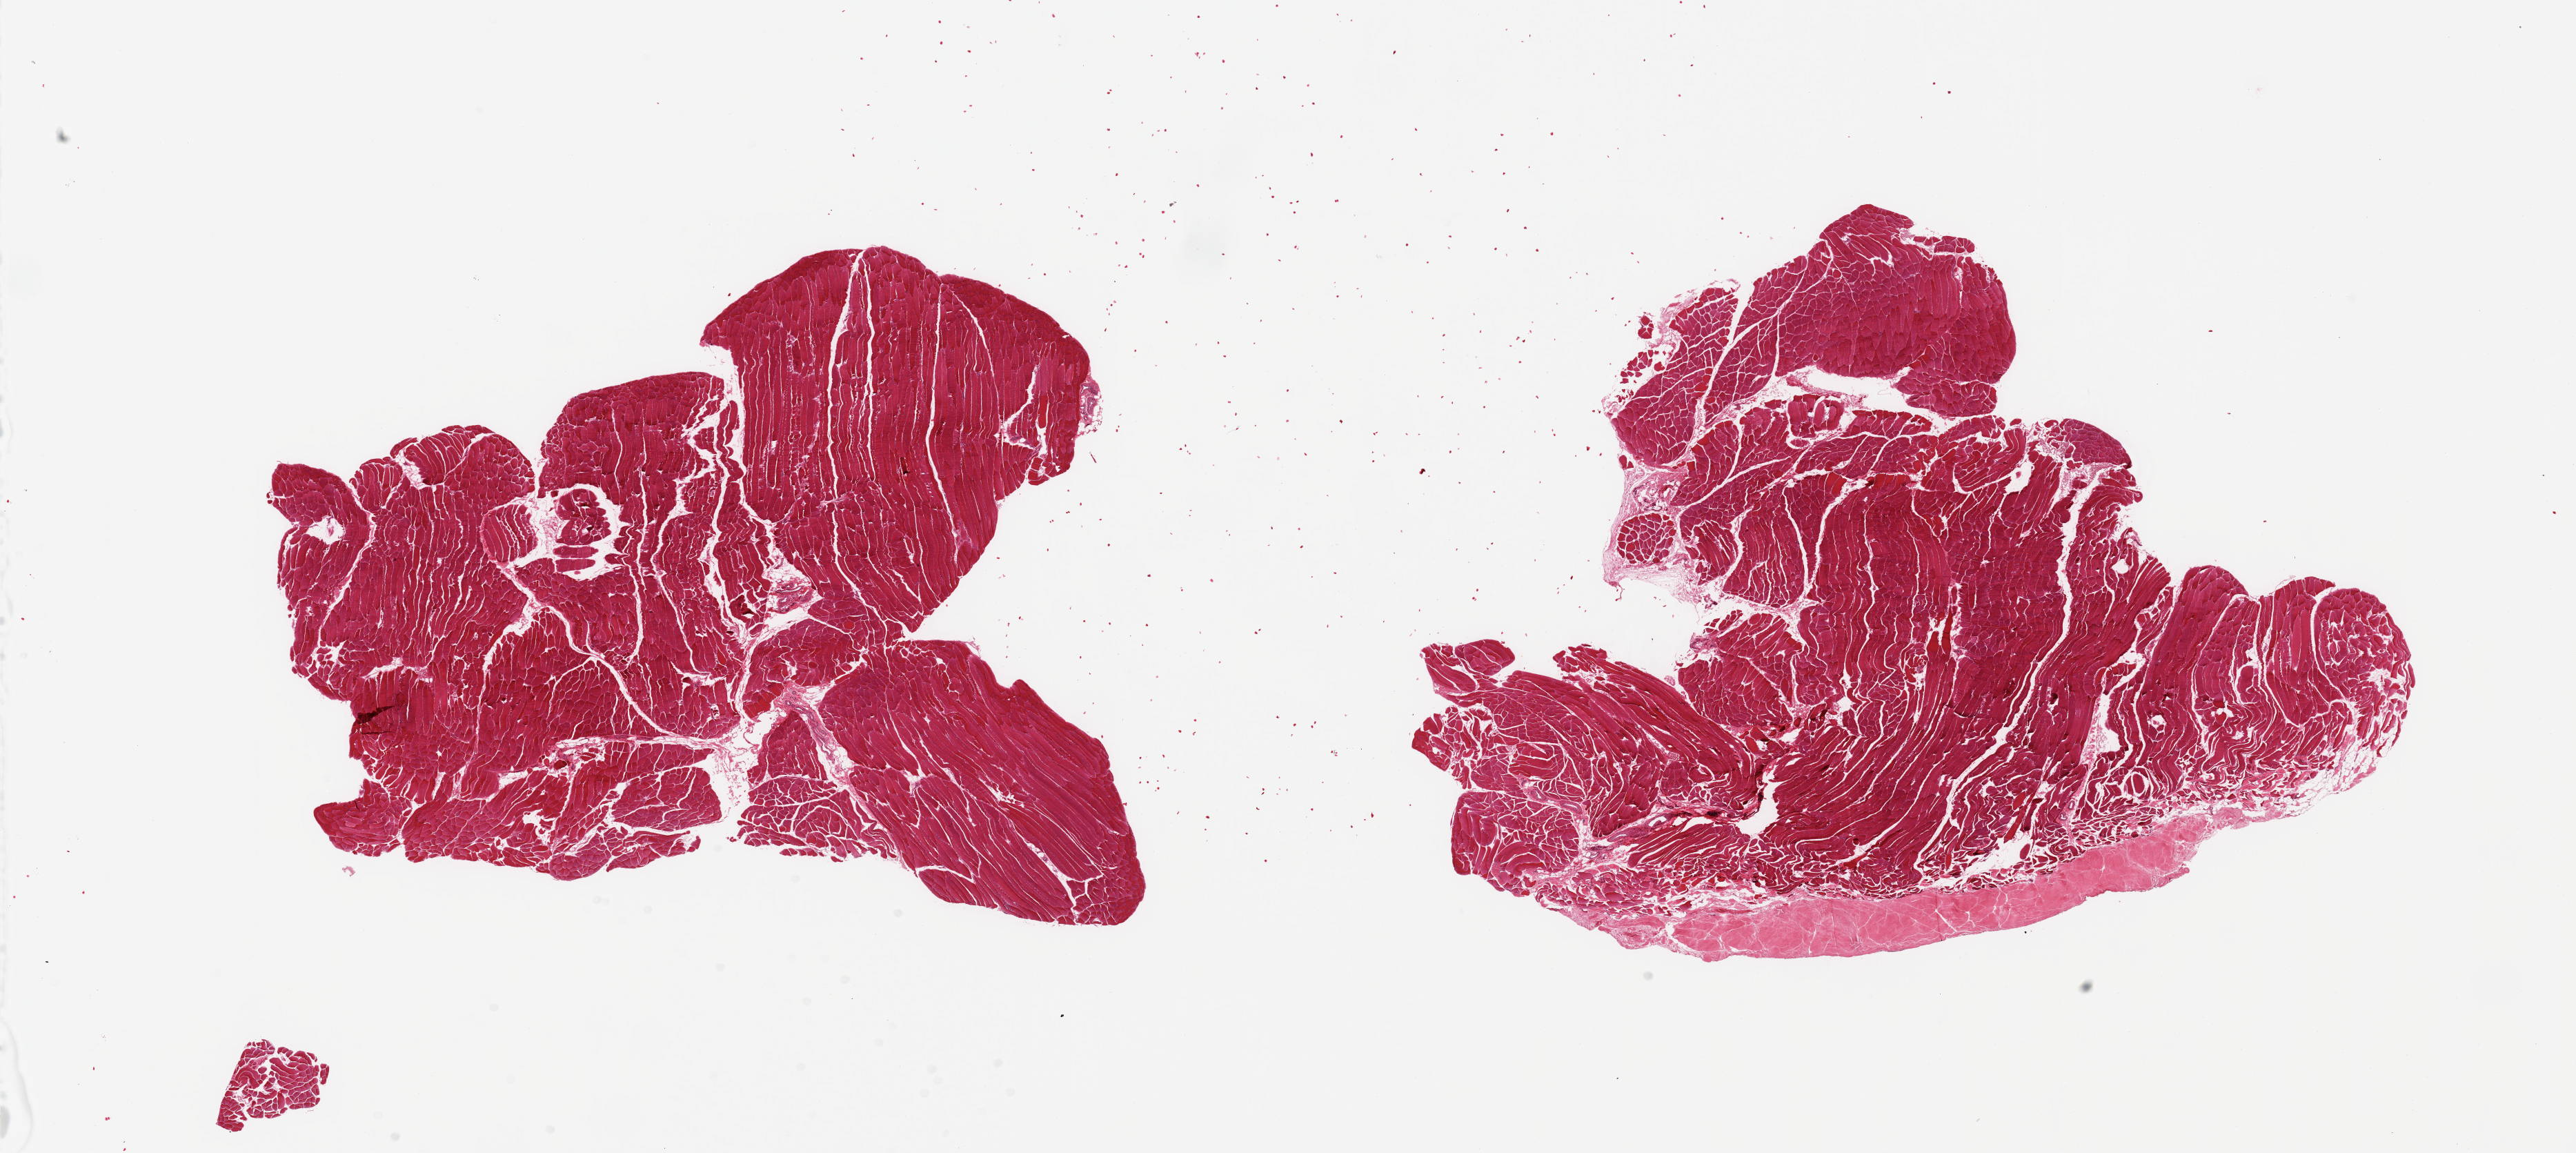
Haematoxylin and eosin whole-slide image, a low-resolution overview of the entire scanned area, about 29.5 x 13.2 mm; PAXgene-fixed, paraffin-embedded tissue; sampled site (target tissue): skeletal muscle; donor tissue sample. Male donor.
- review note (as recorded): 2 pieces; skeletal muscle, portion of tendon